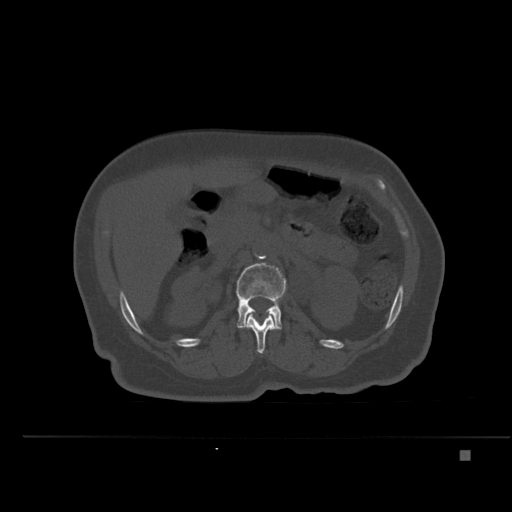
CT including the spine, one axial slice; bone window (W 1800 / L 400 HU); 512 × 512 image matrix, field of view 422 × 422 mm. Female patient, age 74 years. Case-level facts recorded for this patient, not image findings: primary cancer: colon.
Outlined on this slice (semi-automatic segmentation, software-assisted and operator-edited):
- L1 vertebra: bounding box <244,312,277,354> (left, top, right, bottom; pixels)
- L2 vertebra: <236,262,287,330>